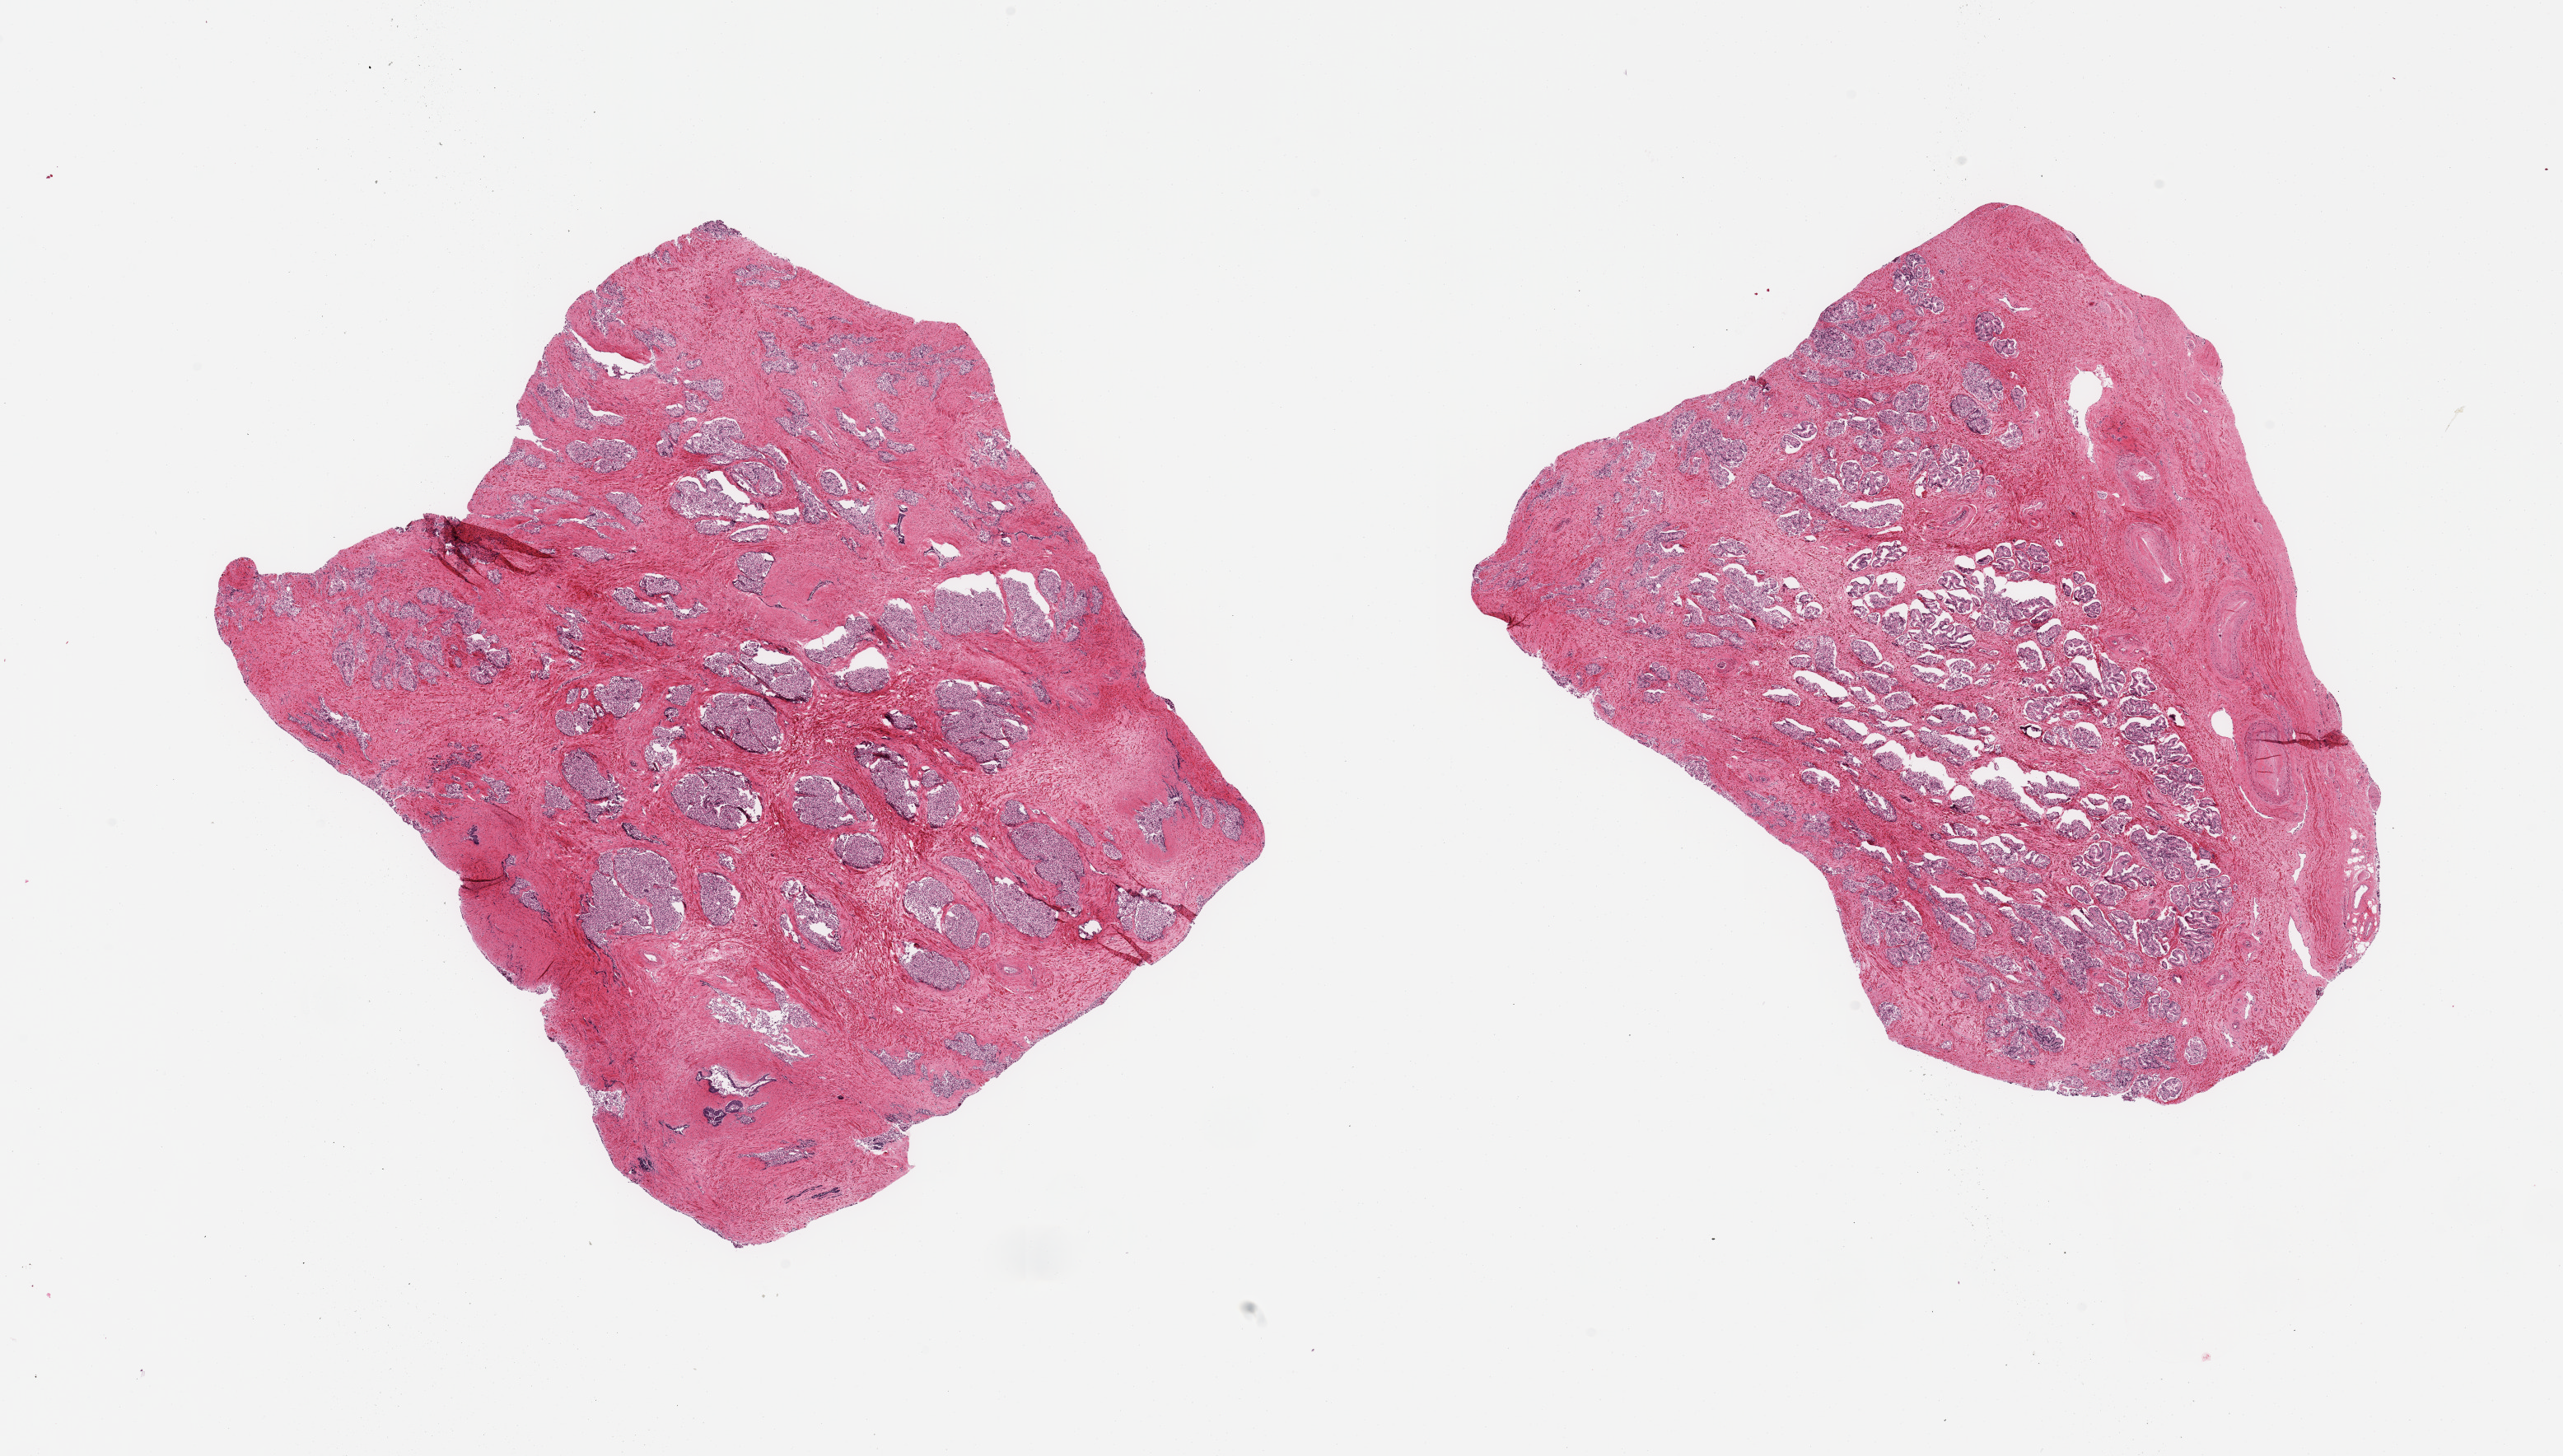
Whole-slide image, H&E stain — shown as a low-resolution overview of the whole scanned area (about 24.6 x 14.0 mm). PAXgene-fixed, paraffin-embedded tissue. Section of prostate (target tissue). Tissue donor sample. Donor sex: male.
Review note (as recorded): 2 pieces, hyperplastic pattern, glandular elements moderate-advanced autolysis.